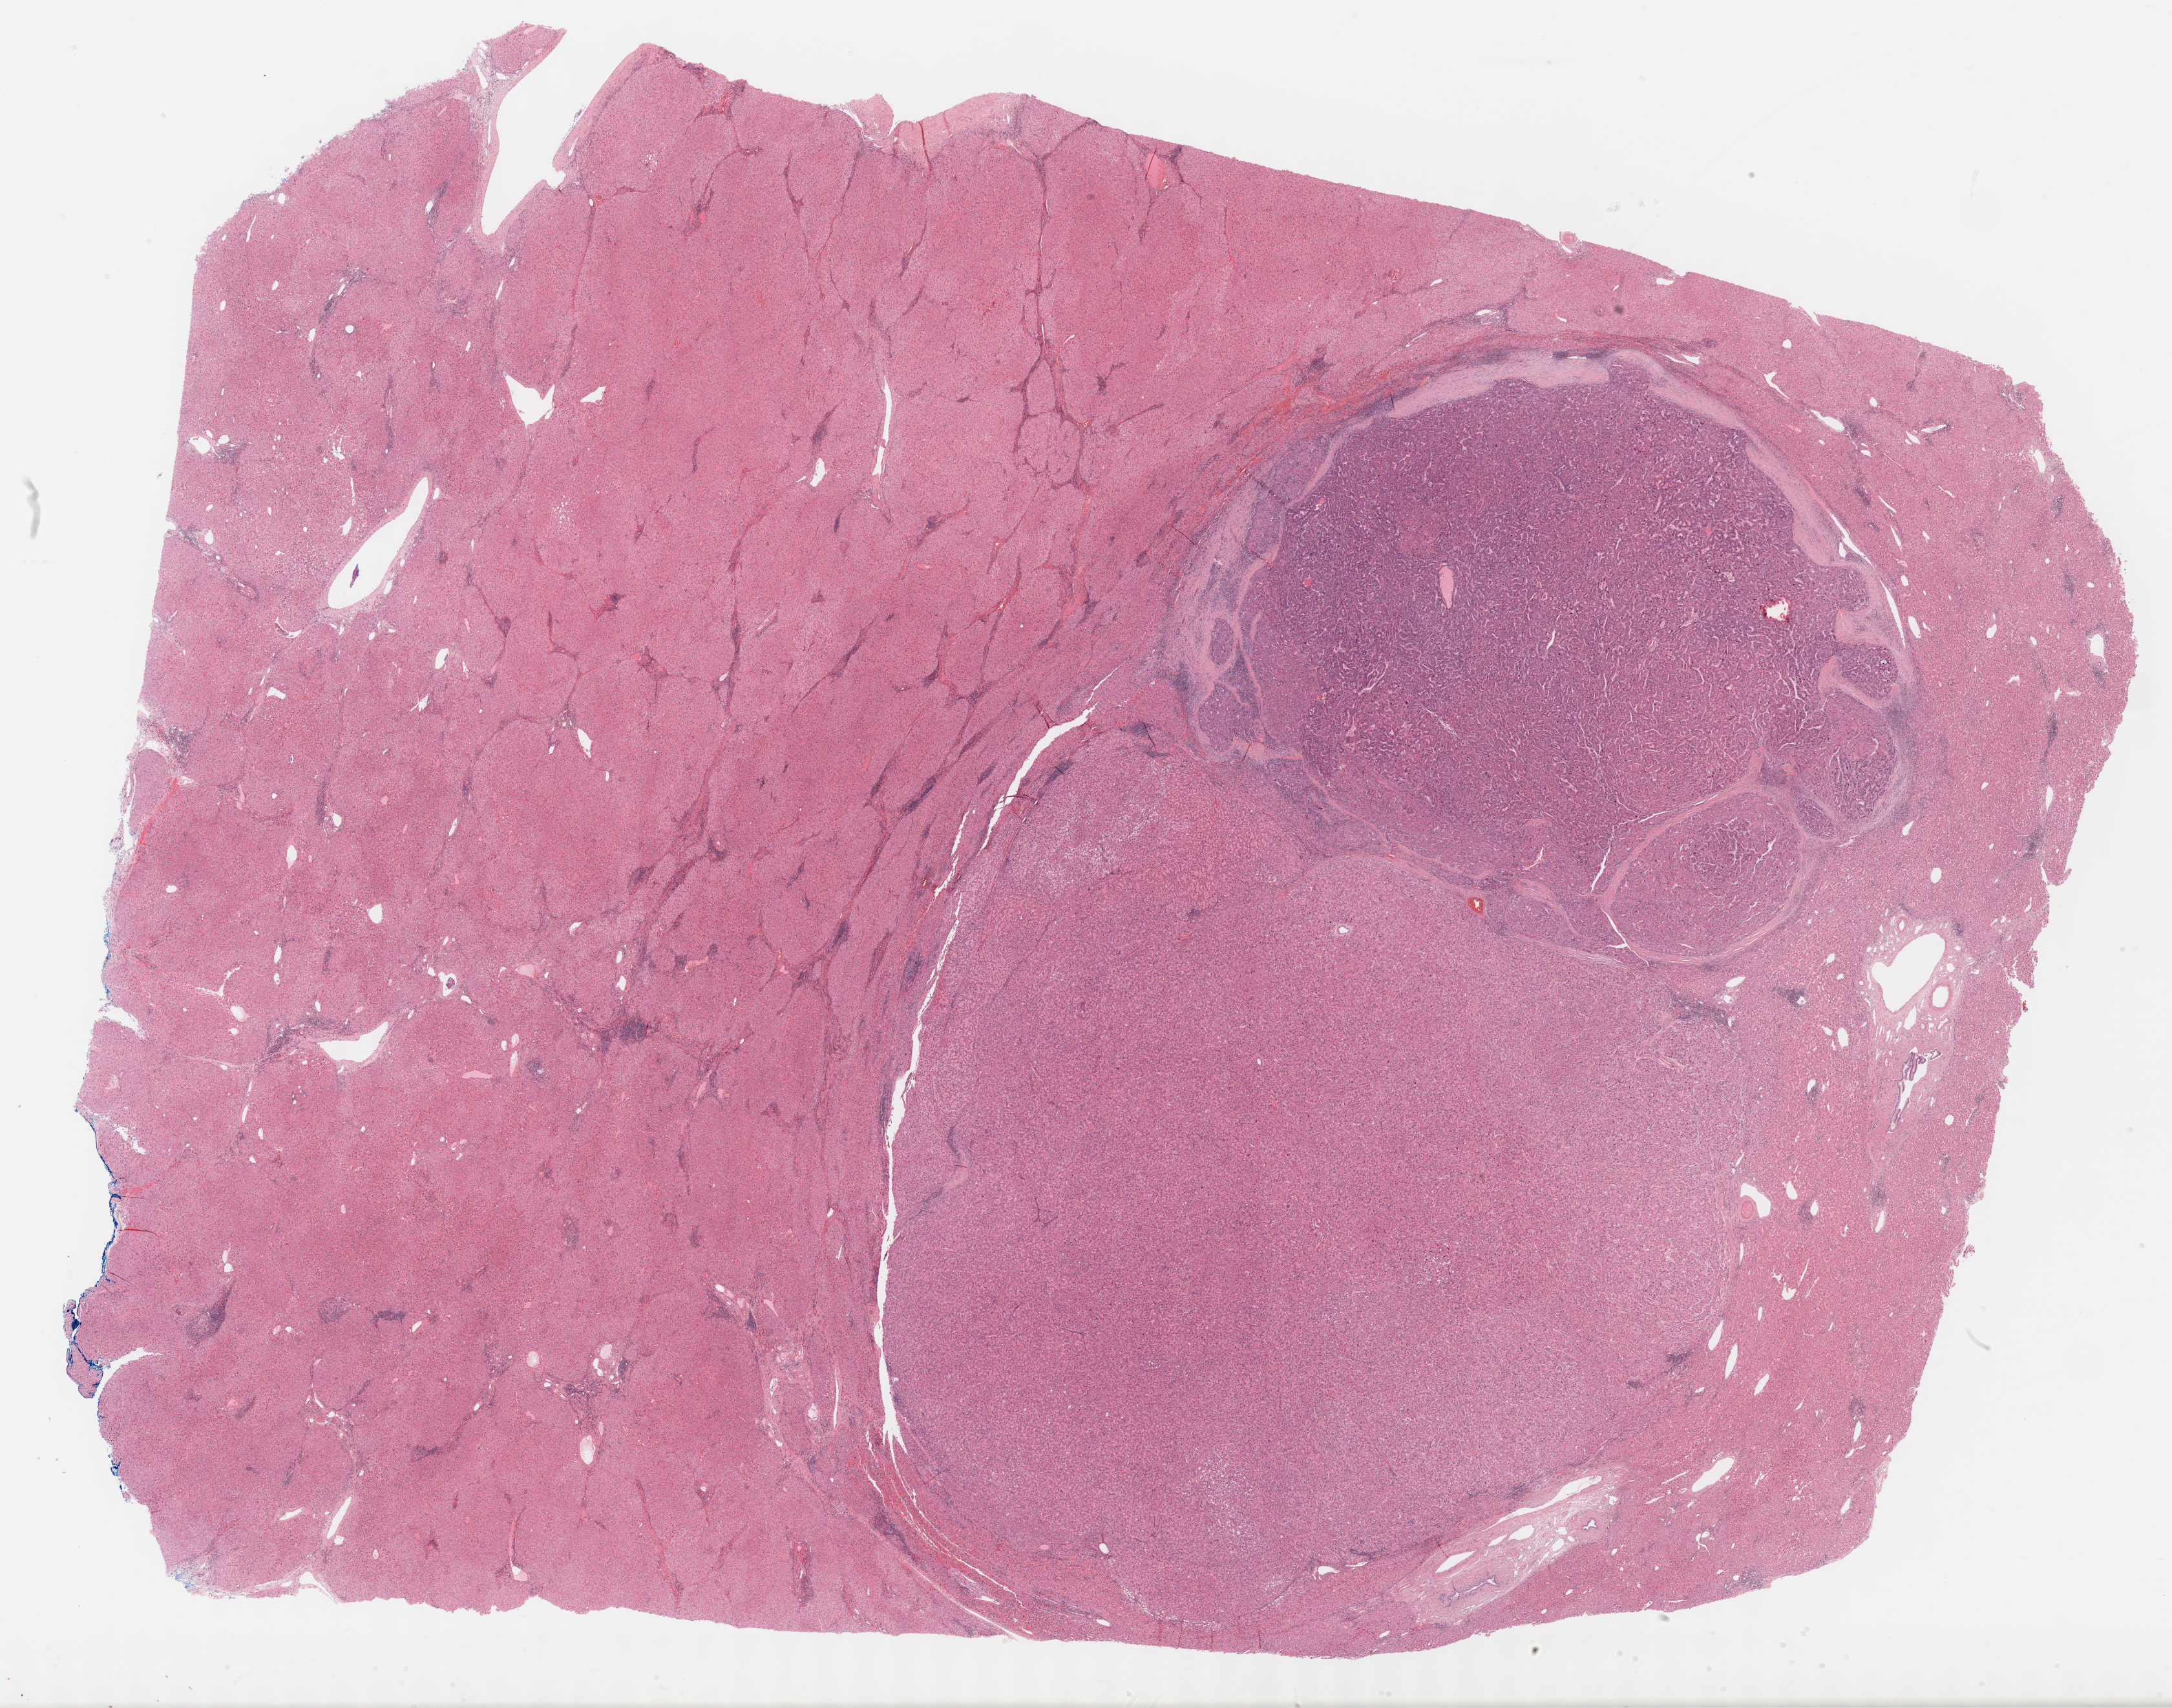
Digitized H&E tissue section (whole slide), a low-resolution overview of the entire scanned area, about 27.2 x 21.4 mm (from a 40x scan), formalin-fixed paraffin-embedded (FFPE) diagnostic section, primary tumour sample from the liver. Patient: male, age at initial diagnosis 58 years.
Histologic diagnosis: Hepatocellular carcinoma, NOS.